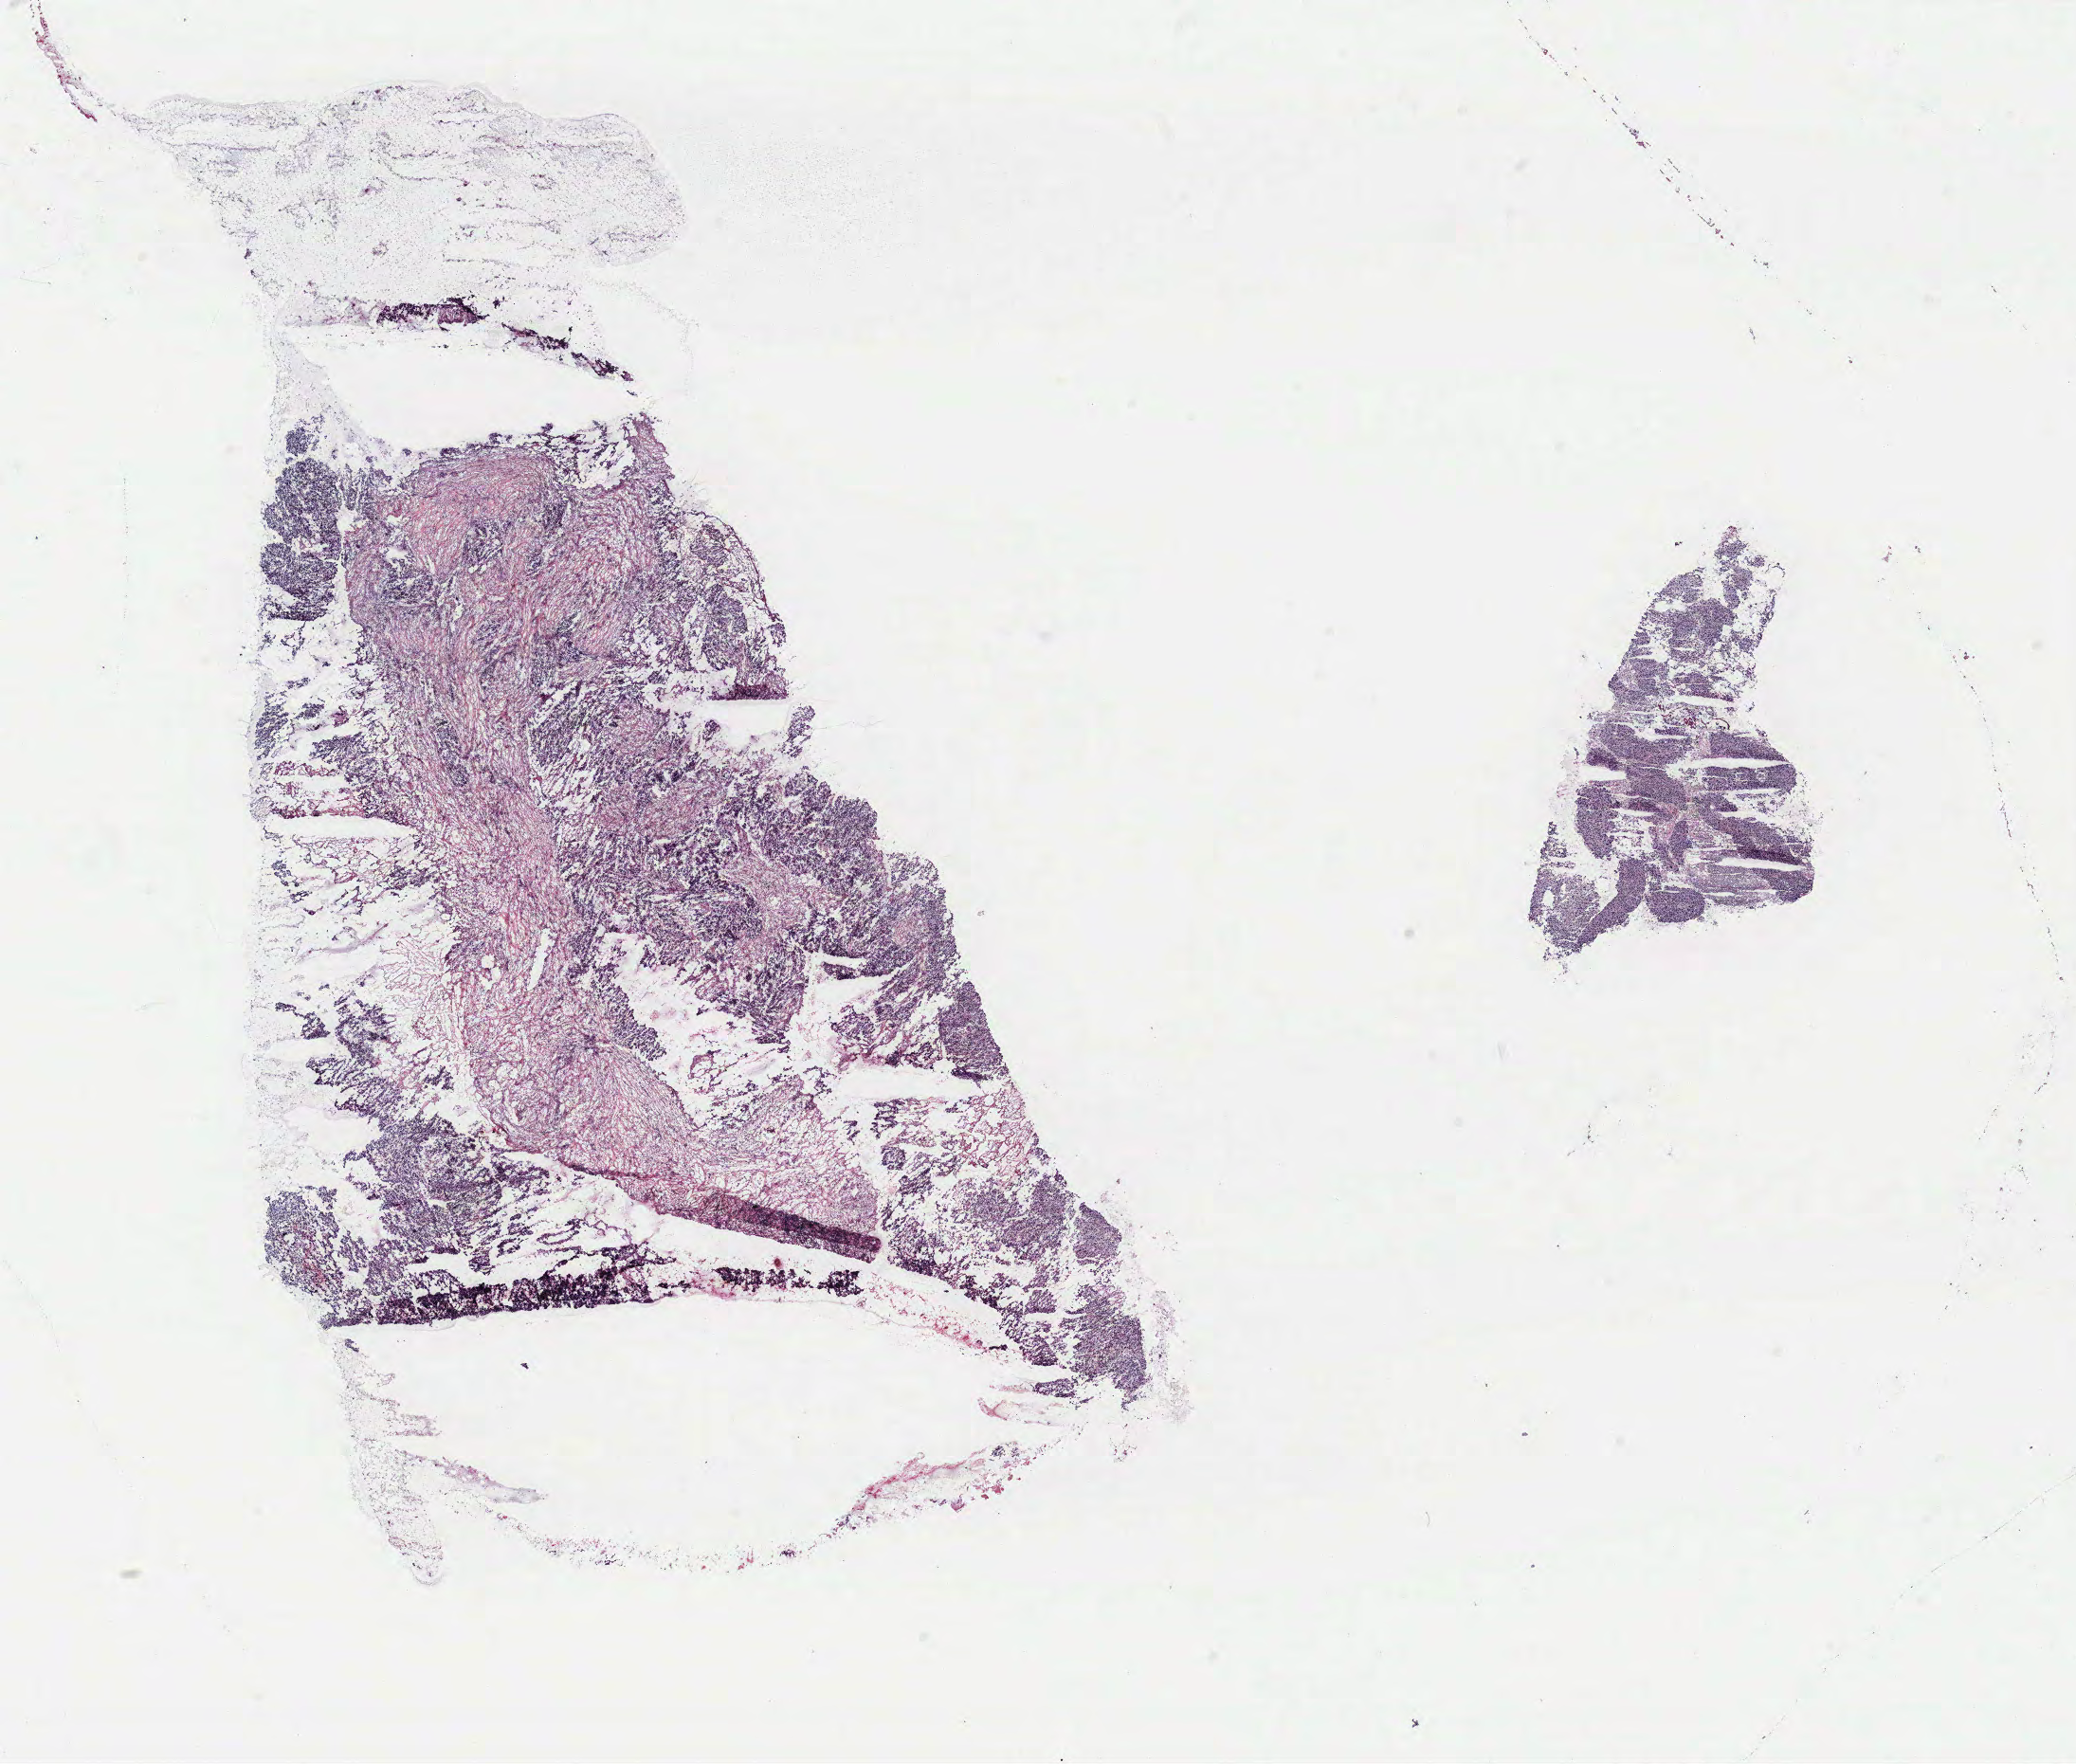
Digitized Hematoxylin and eosin (H&E) stained tissue section (whole slide) — whole scanned area (about 17.5 x 14.9 mm) shown as a low-resolution overview; breast, tissue type not recorded. Female, 65 y/o.
Patient diagnosis: Infiltrating duct carcinoma, NOS.